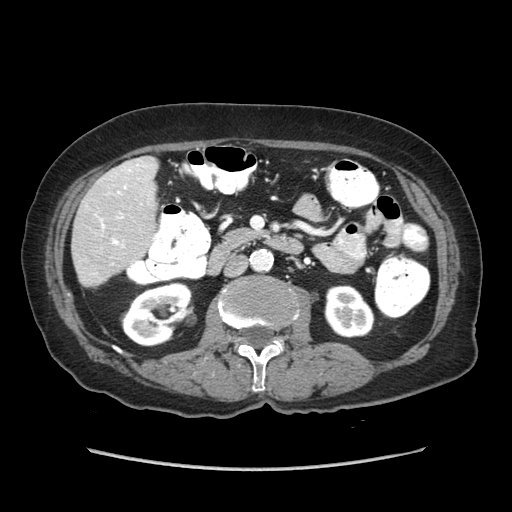
Contrast-enhanced abdominal CT (liver protocol), one axial slice; slice 20 of 89 in the series (ordered by position); soft-tissue window (W 400 / L 40 HU); 512 × 512 image matrix. Case-level facts recorded for this patient, not image findings: diagnosis: hepatocellular carcinoma (patient treated with transarterial chemoembolisation; whether this scan precedes or follows treatment is not stated here); TNM stage (as recorded): Stage-IIIA; Child-Pugh class: A; tumour differentiation: well differentiated; tumour size: 11 cm.
Structures marked on this image (semi-automatically segmented with operator editing):
- liver parenchyma outside the tumour (the mass and vessels are separate outlines, so this box may not span the whole liver): bounding box [x1, y1, x2, y2] px = [72, 156, 158, 286]
- liver vessels: [97, 164, 146, 247]